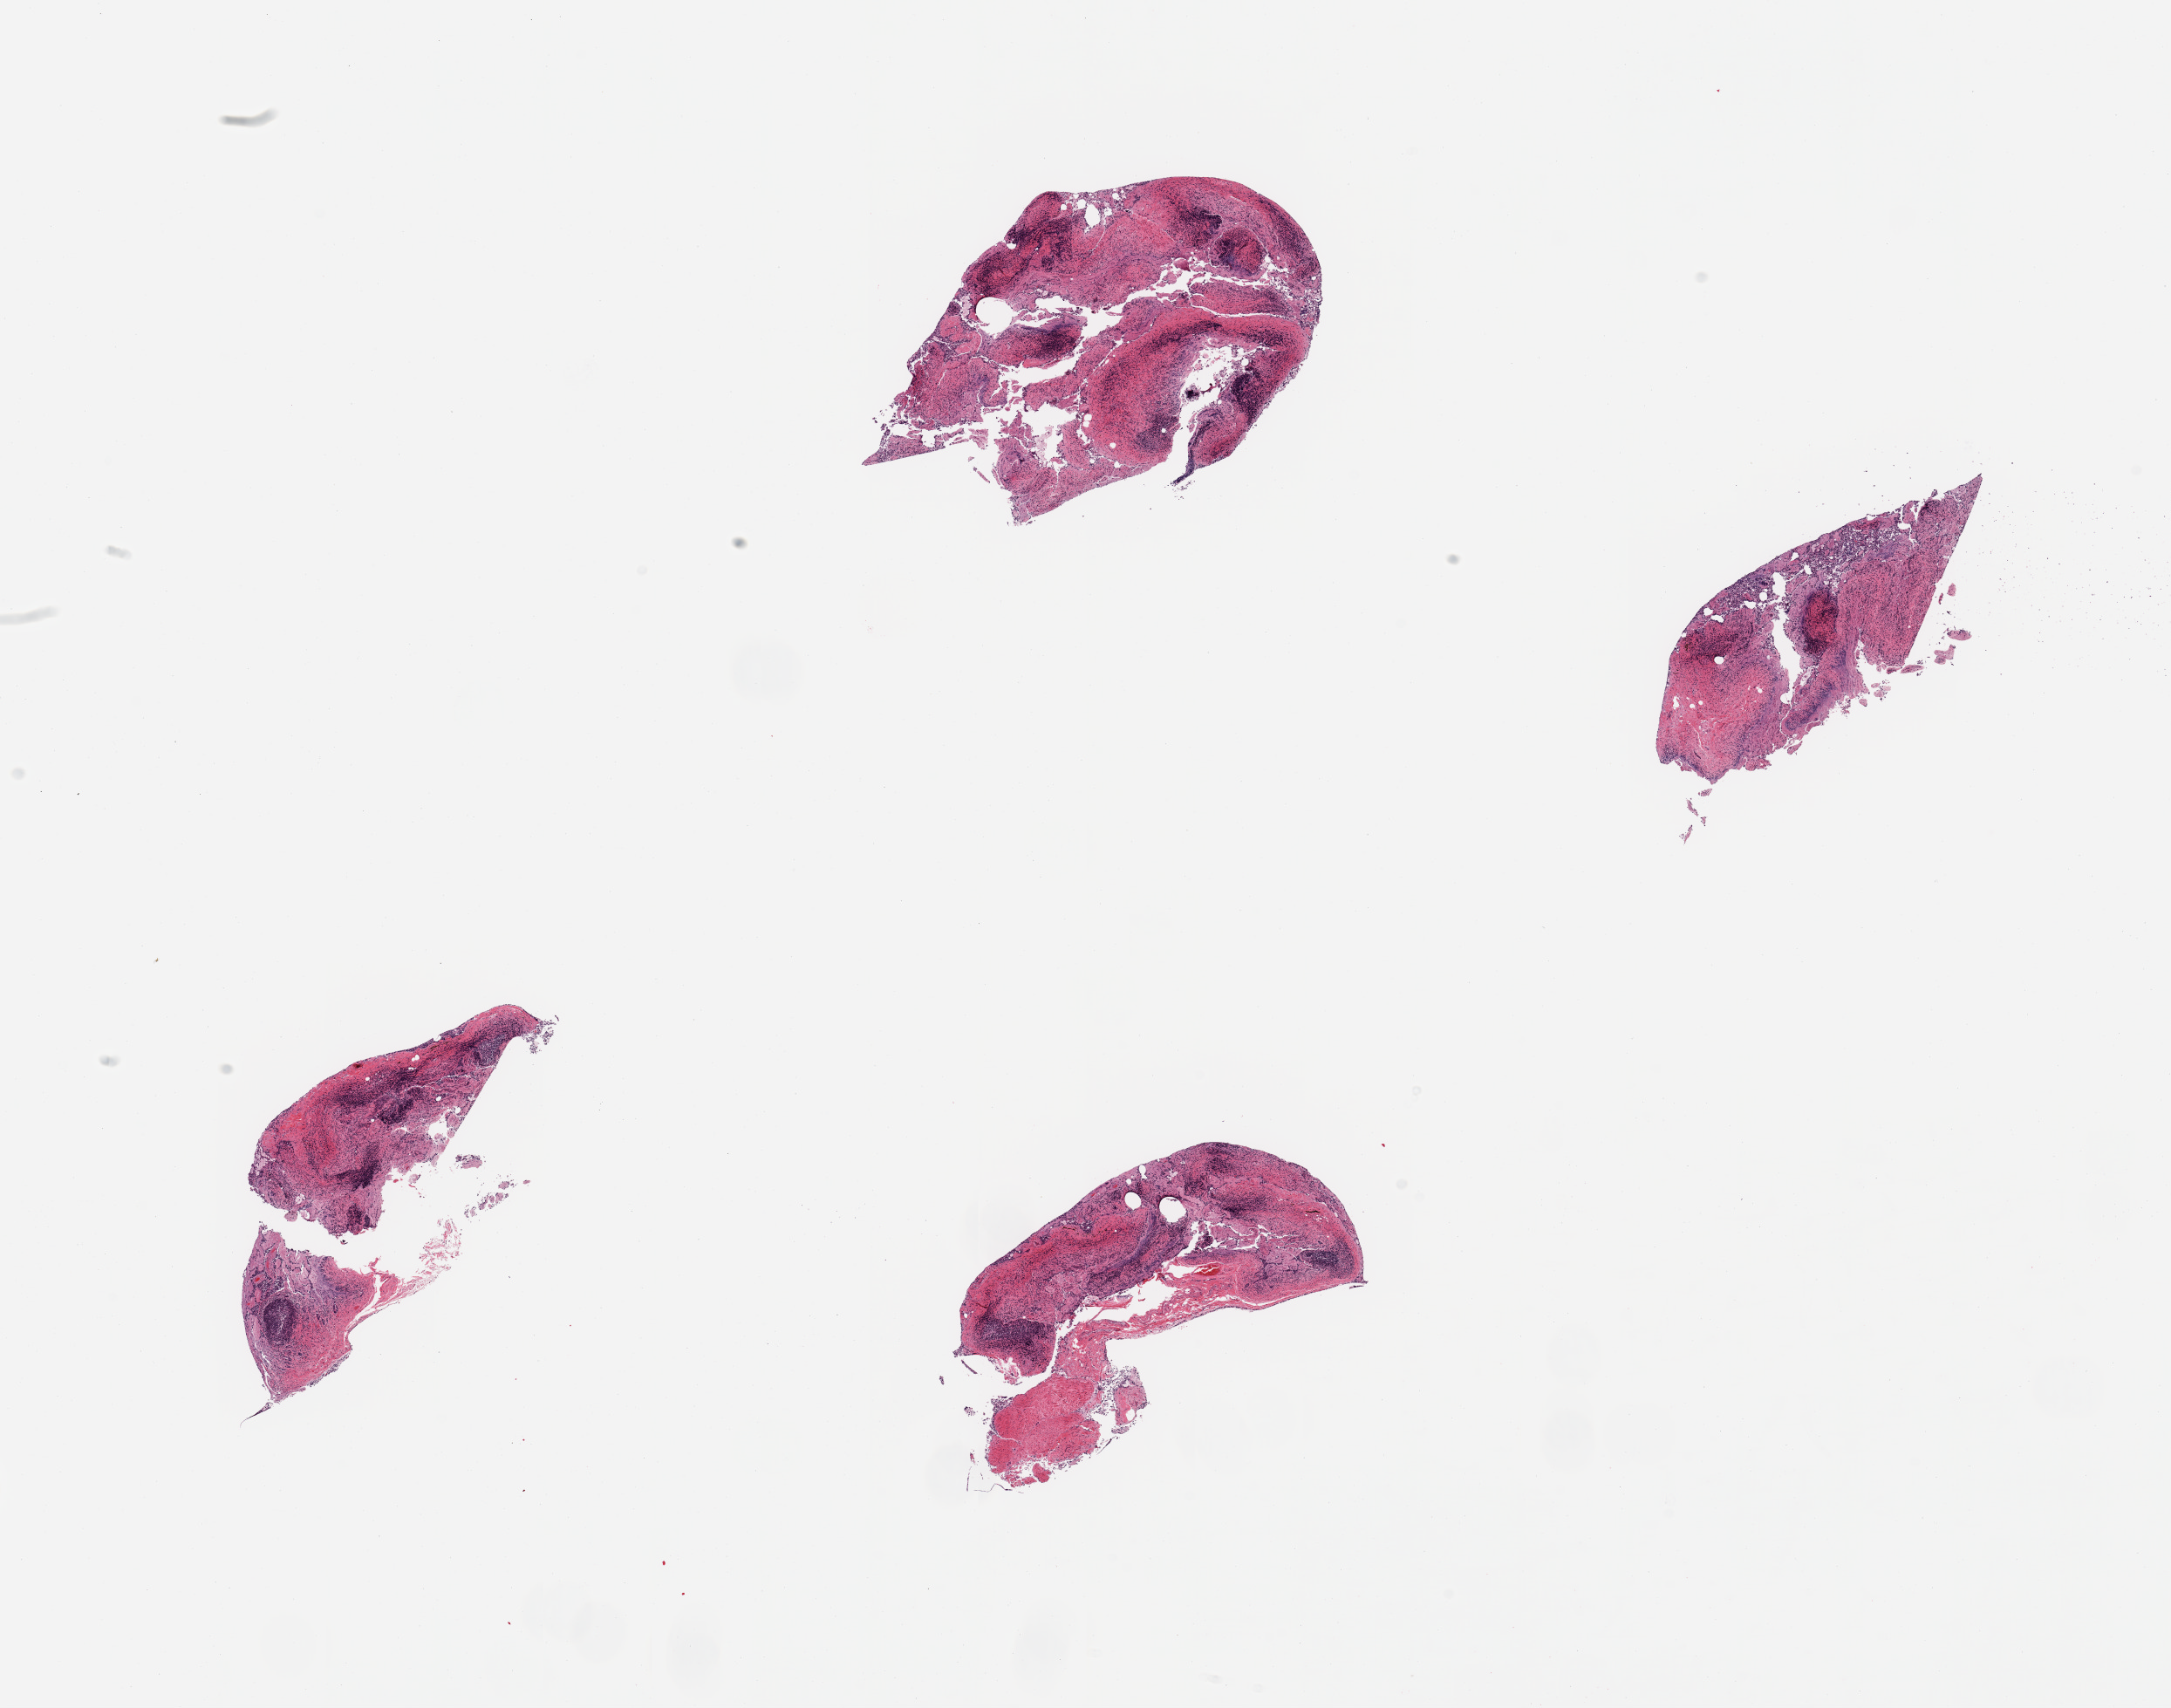
Whole-slide image, H&E stain, a low-resolution overview of the entire scanned area, about 19.7 x 15.5 mm (acquisition: 20x scan). Donor sex: male.
Specimen: PAXgene-fixed paraffin-embedded (PFPE) section; sampled site (target tissue): ileum; donor tissue sample.